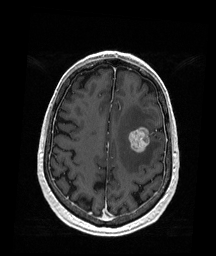
Brain MRI from a brain-tumour surgery series, one axial slice. T1-weighted post-contrast. 216 × 256 image matrix, field of view 211 × 250 mm. From the clinical record (not read from this slice): histopathology: Metastatic Melanoma; tumour location: Left Frontal.
Annotated regions visible in this slice (manually delineated by an expert):
- tumour: bounding box [x1, y1, x2, y2] px = [129, 127, 151, 153]